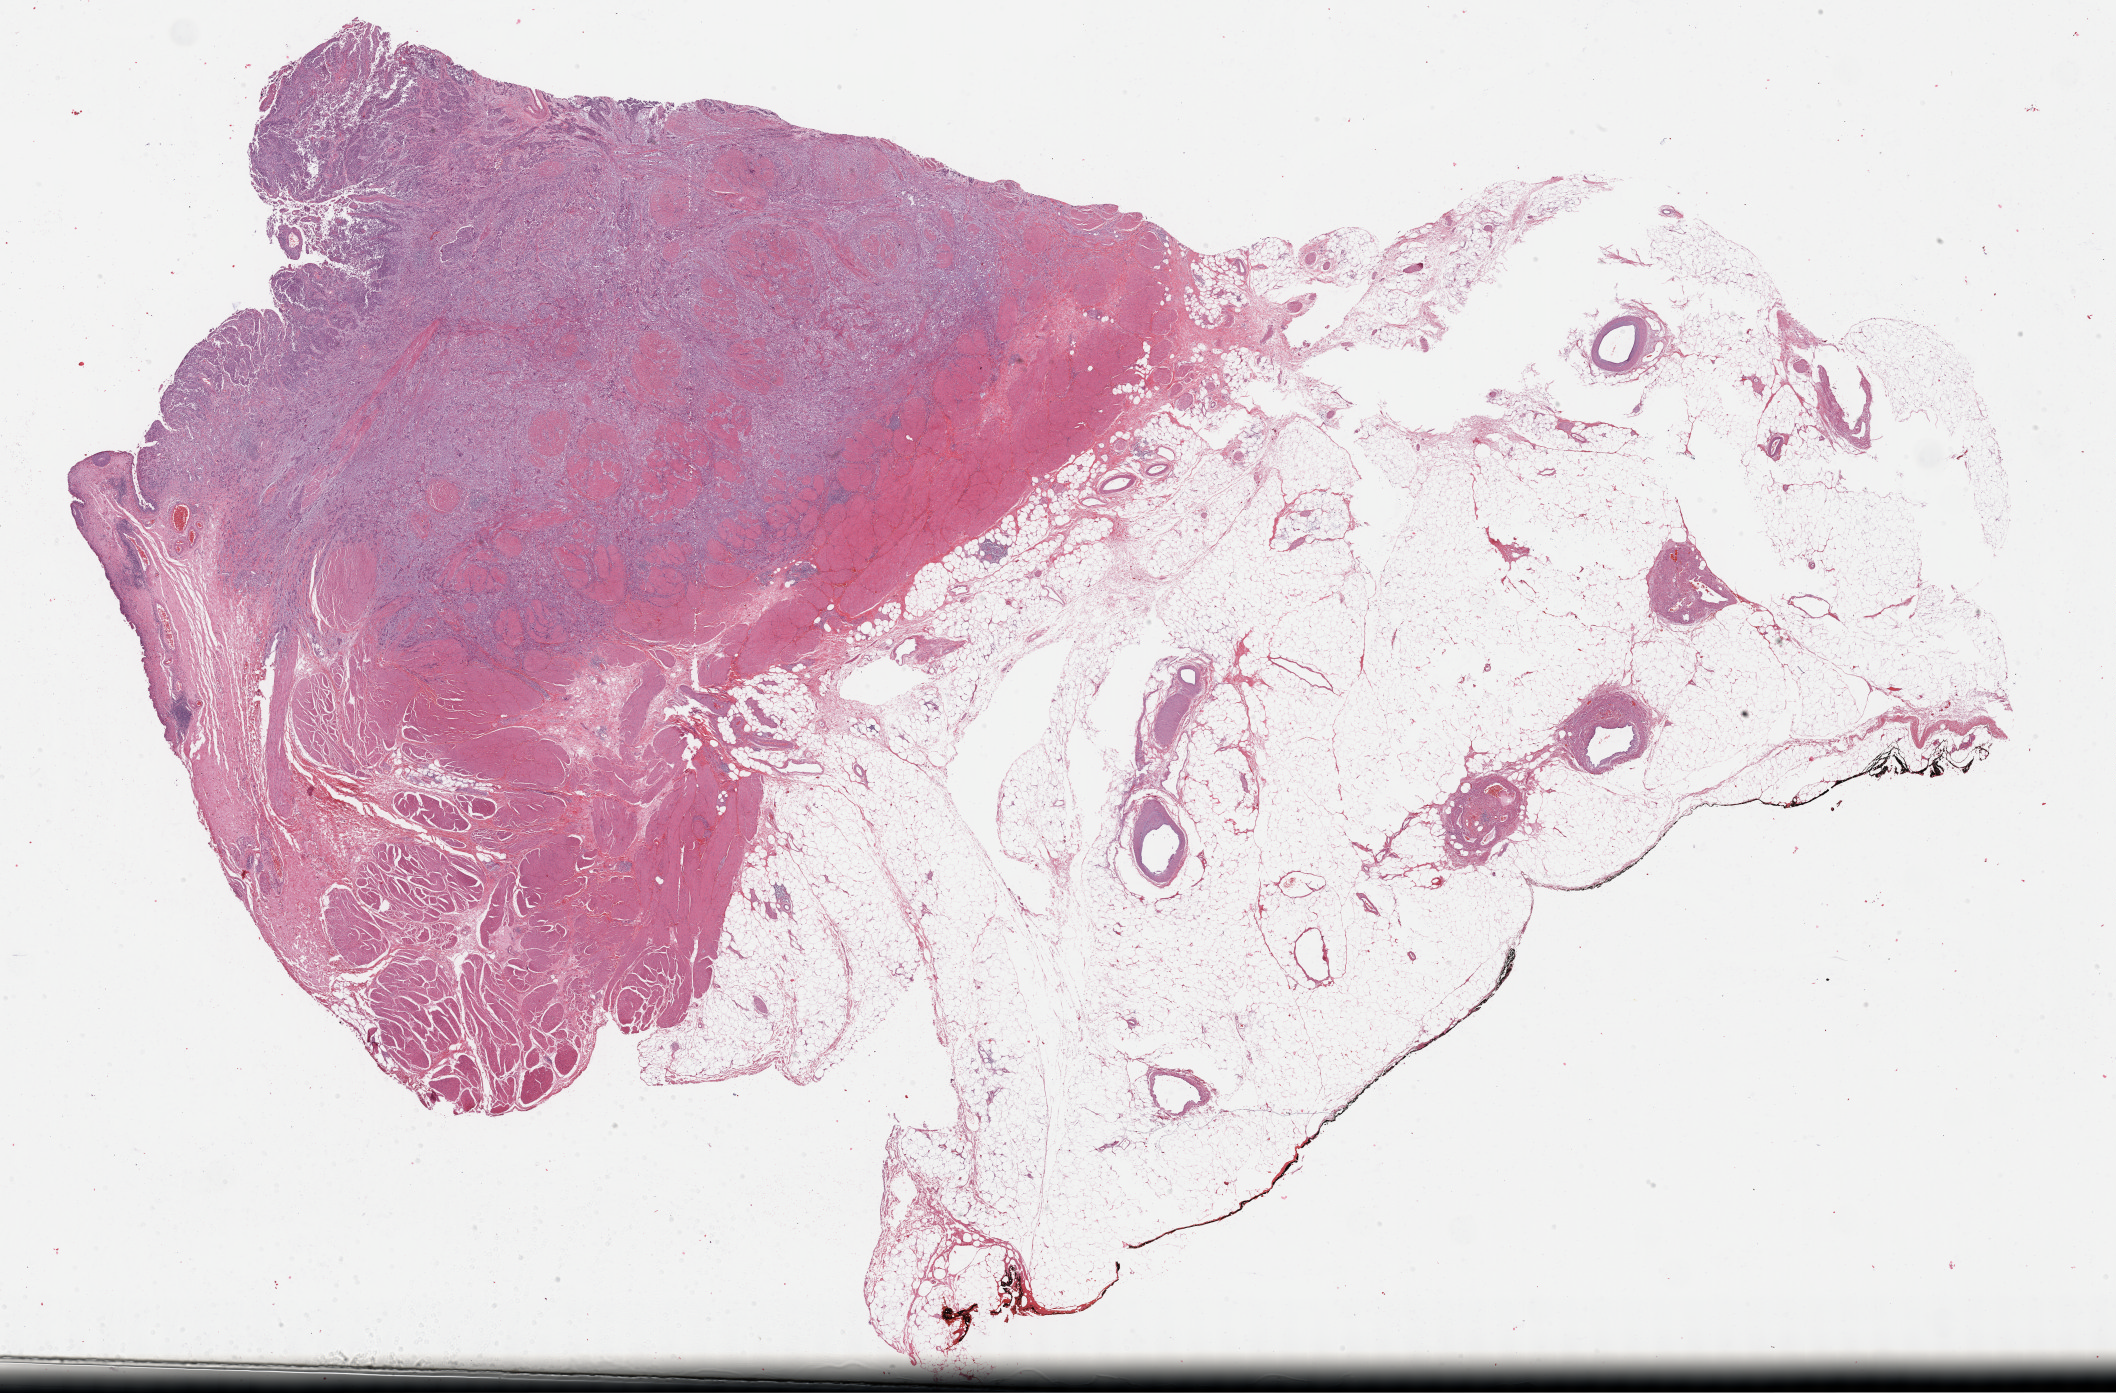
Whole-slide histology image, Hematoxylin and eosin (H&E) stained — whole scanned area (about 34.2 x 22.5 mm) shown as a low-resolution overview, formalin-fixed paraffin-embedded (FFPE) diagnostic section, bladder, primary tumour sample. Male patient; age at initial diagnosis 59 years. Histologic grade: high grade.
- pathologic diagnosis: Transitional cell carcinoma
- lymph nodes positive (case pathology): 0 of 41 examined
- AJCC pathologic stage: III (6th edition)